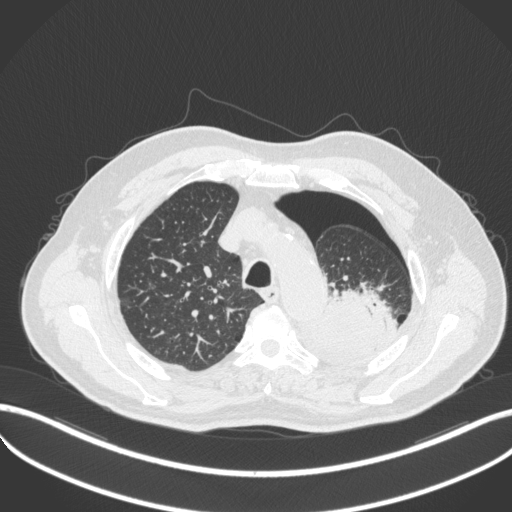
Chest CT, one axial slice. Position 392 of 466 along the scan axis. Reconstruction kernel B31f. Lung window (W 1500 / L -600 HU). 1 mm slice thickness. 512 × 512 image matrix, field of view 400 × 400 mm. Male patient, age 76 years. Case-level facts recorded for this patient, not image findings: clinical TNM (as recorded): T3 N0 M1b.
Structures marked on this image (bounding box drawn by a radiologist):
- lung tumour (recorded histology: adenocarcinoma): box from (x=315, y=289) to (x=382, y=361) px